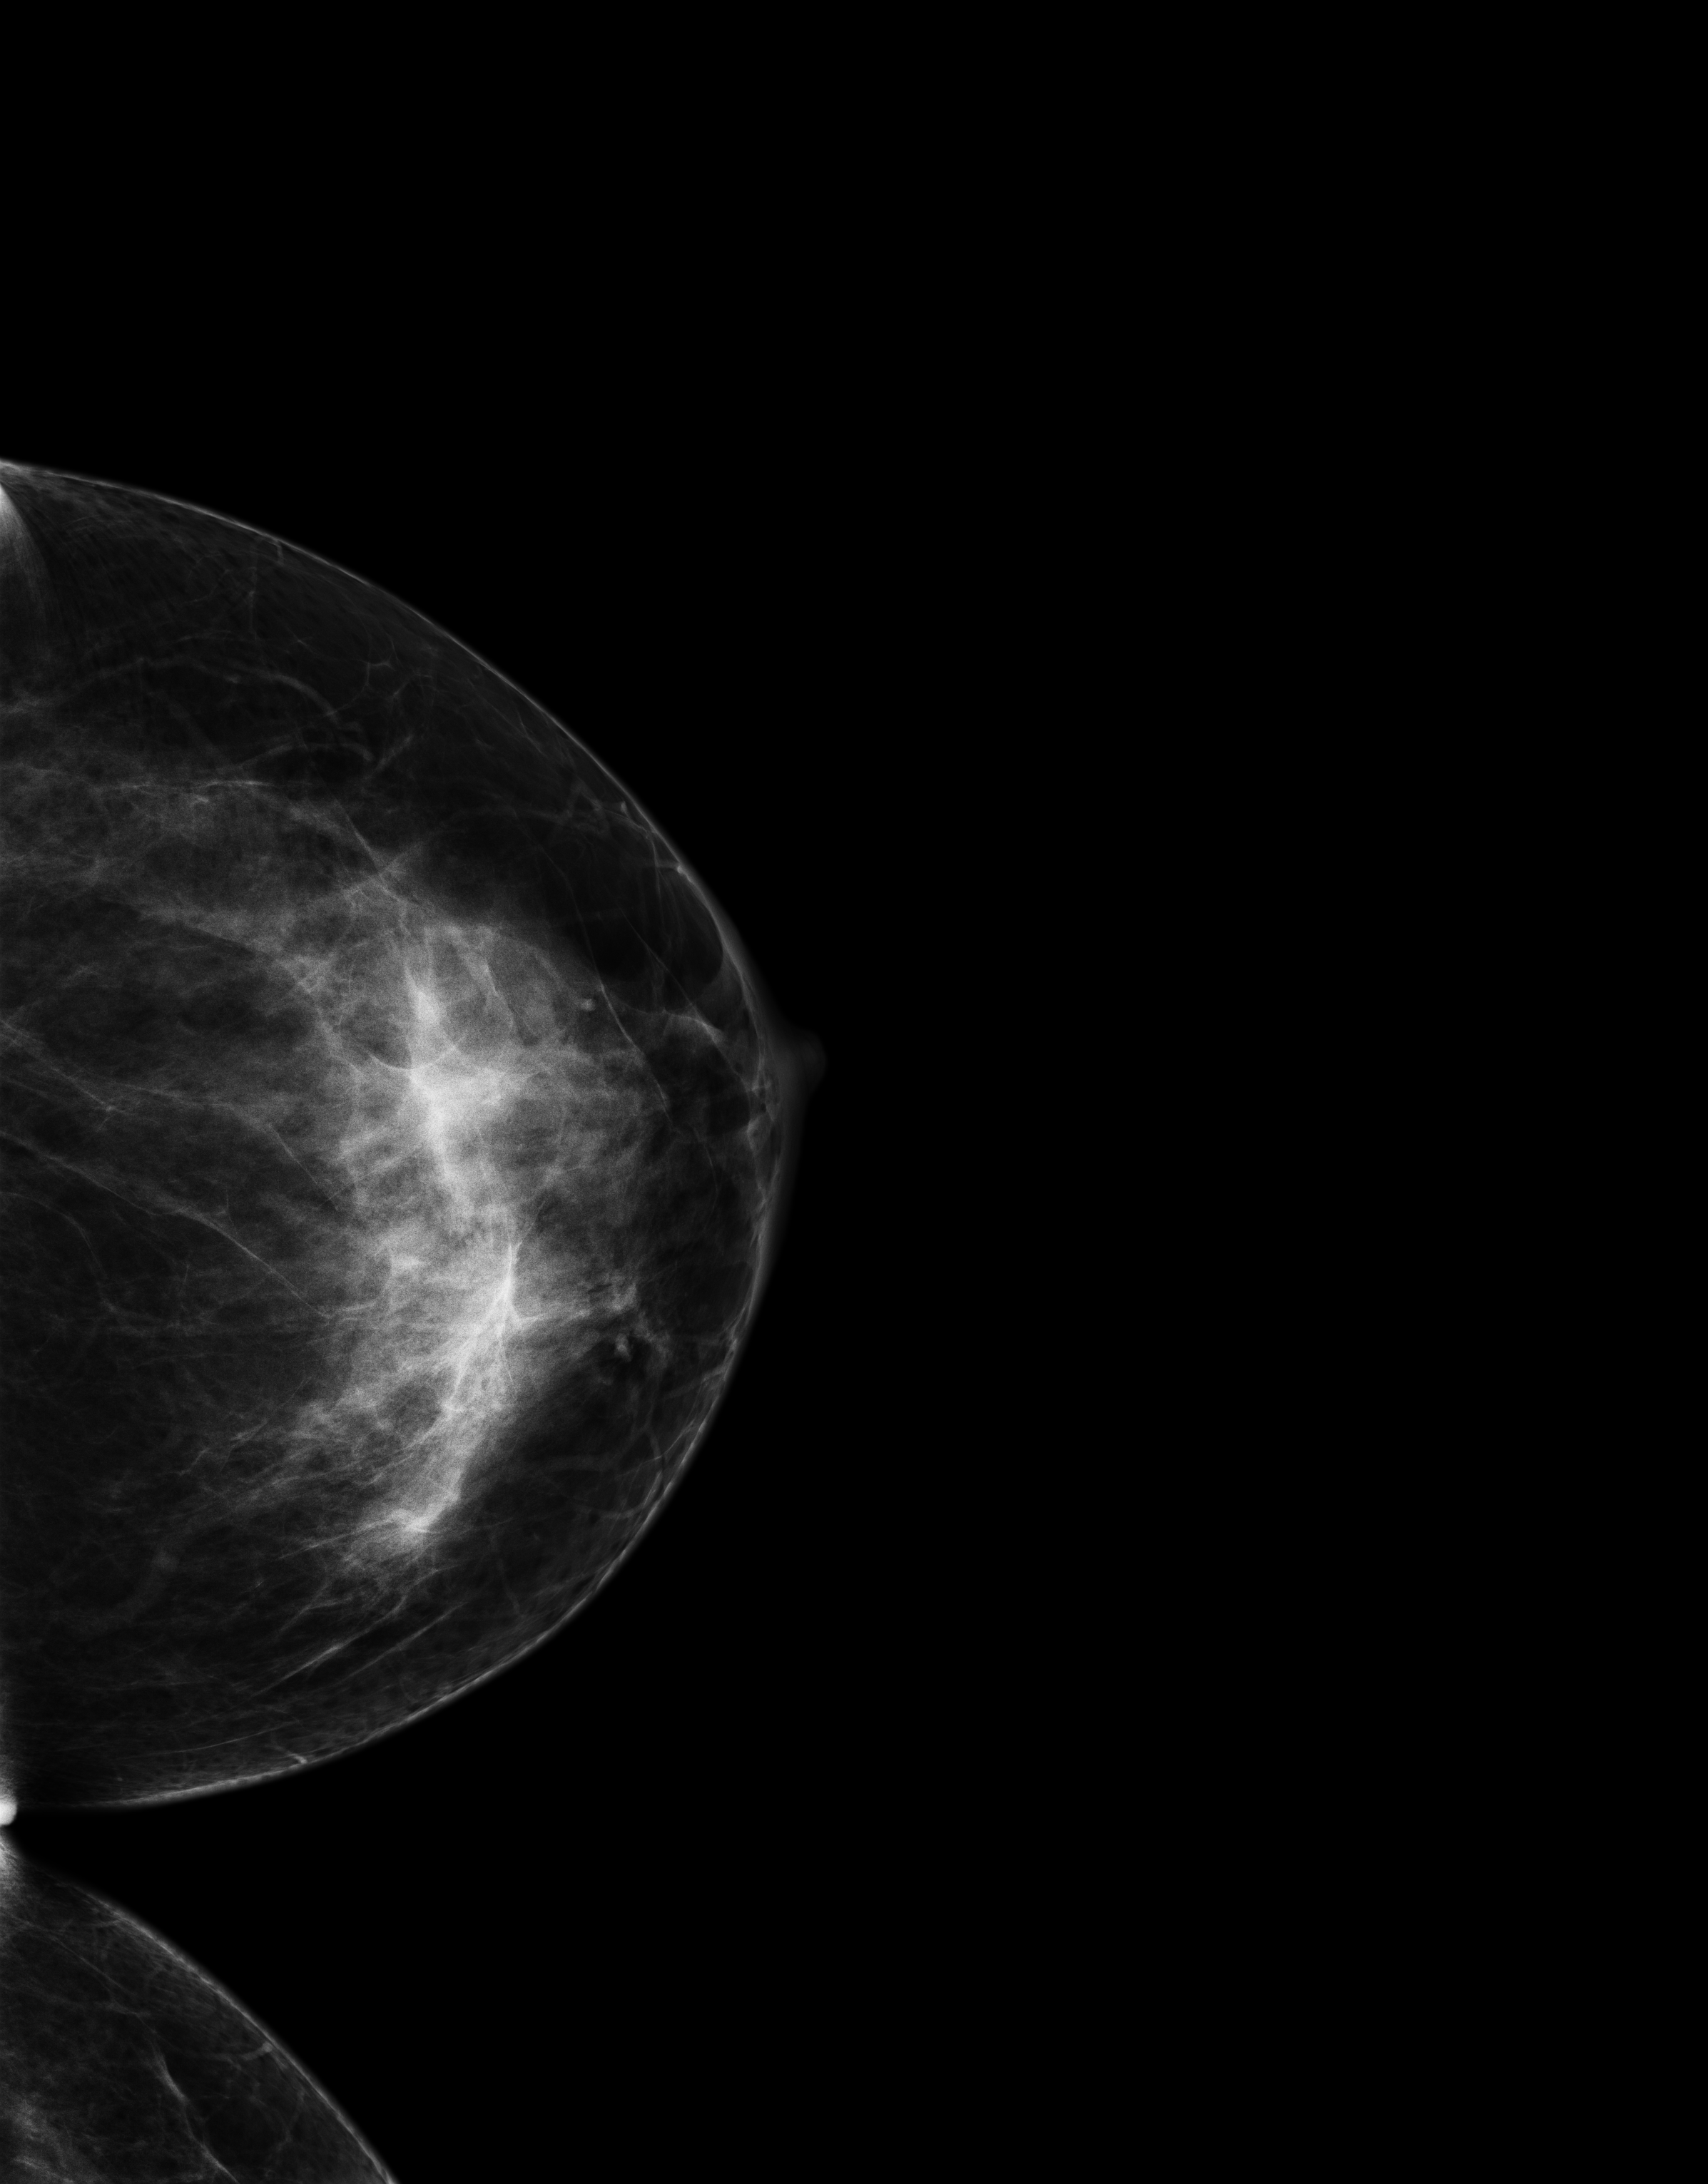
Digital mammogram (FFDM), left breast, CC view, annual screening mammography examination, system: Senographe Essential ADS_56.21.3. Patient: female, 44 years.
BI-RADS breast density category at the screening exam (both breasts, scale 1–4): 3. Final BI-RADS category for the screening round (tomosynthesis exam, both breasts): category 1. Recall: no recall after this screen.